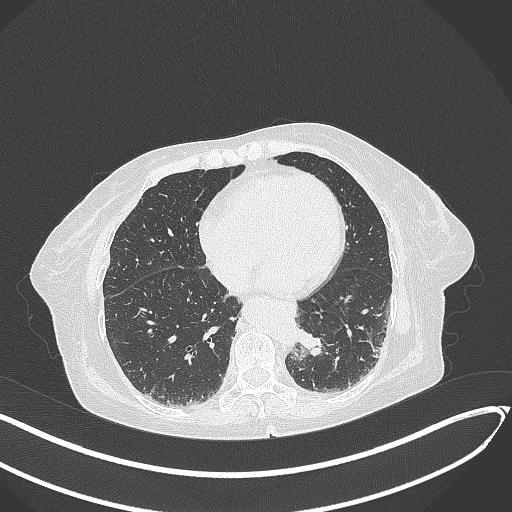
Chest CT, one axial slice. Position 70 of 324 along the scan axis. Reconstruction kernel B70f. 120 kVp. Lung window (W 1500 / L -600 HU). 1 mm slice thickness. 512 × 512 image matrix, field of view 400 × 400 mm. Female patient, age 82 years. Case-level facts recorded for this patient, not image findings: clinical TNM (as recorded): T1b N0 M1.
Annotated regions visible in this slice (bounding box drawn by a radiologist):
- lung tumour (recorded histology: adenocarcinoma): bounding box (x1, y1, x2, y2) in pixels: (294, 321, 326, 368)